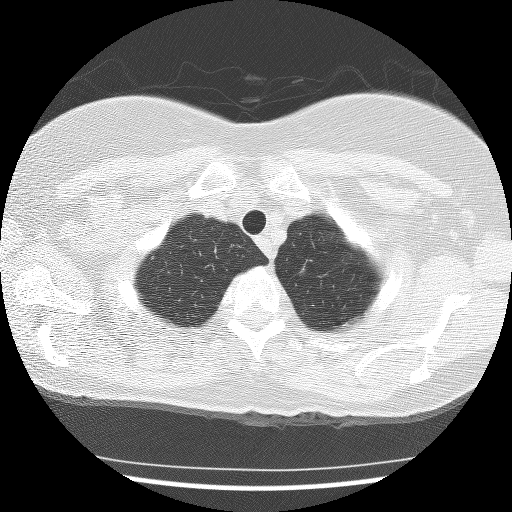
Chest CT (low-dose screening protocol), one axial image, baseline screening round, lung window (W 1500 / L -600 HU), lung (sharp) reconstruction kernel (BONE), slice 13 of 120 in the series, 512 × 512 image matrix, field of view 320 × 320 mm. Female, age 59 years at enrolment. Former smoker at enrolment.
Expert reader's lesion annotation, bounding box (x1, y1, x2, y2) in pixels: (281, 256, 321, 290). The screening reader recorded 3 non-calcified nodules or masses ≥4 mm on this exam (left upper lobe, right upper lobe, right upper lobe); which of them this box marks is not recorded. Official screen result: positive, change unspecified: nodule(s) >= 4 mm or enlarging nodule(s), mass(es), or other non-specific abnormalities suspicious for lung cancer.